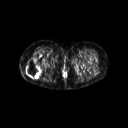
FDG PET of an extremity soft-tissue mass (from a PET/CT study), one axial slice. Position 29 of 267 along the scan axis. 3.27 mm slice thickness. 128 × 128 image matrix, field of view 600 × 600 mm. Female patient, age 57 years. From the clinical record (not read from this slice): histological type: epithelioid sarcoma with vascular differentiation; site of the primary tumour: right buttock.
Structures marked on this image (expert contour drawn on MRI and transferred to this co-registered scan by the dataset authors):
- gross tumour volume (mass): bounding box <25,59,42,77> (left, top, right, bottom; pixels)